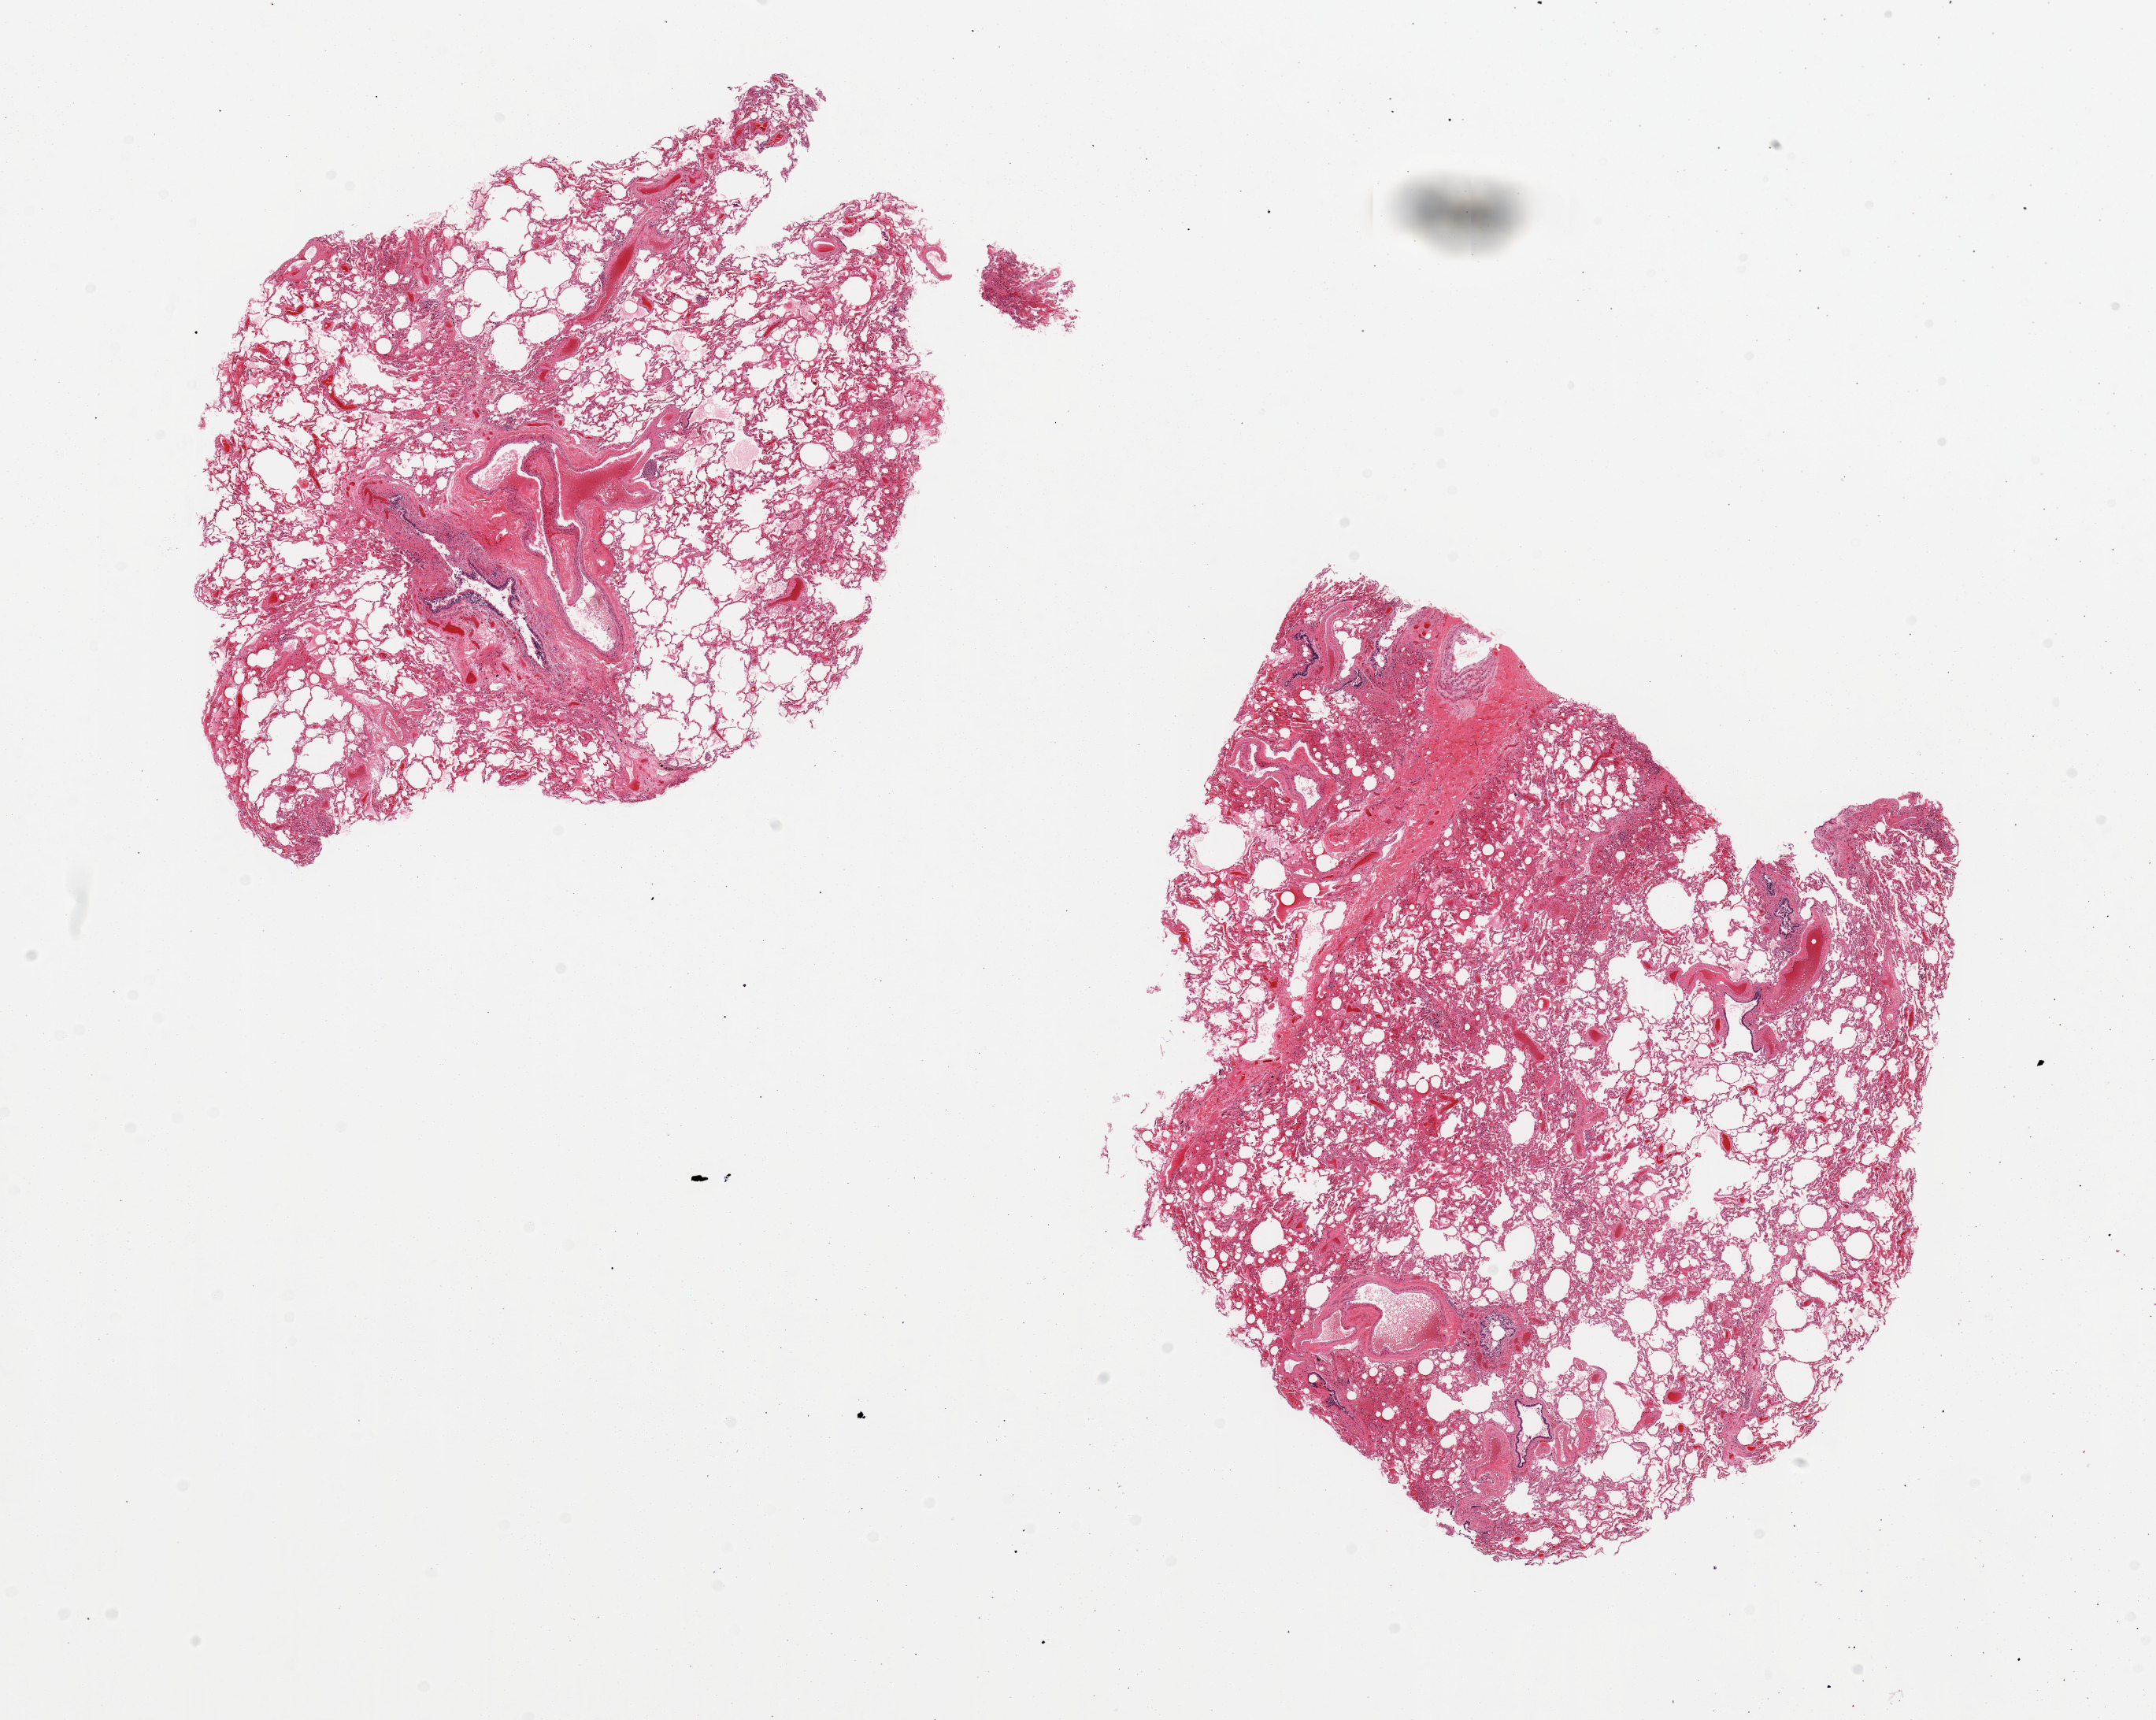
Whole-slide image, H&E stain, brightfield, whole scanned area (about 21.7 x 17.3 mm, from a 20x scan) shown as a low-resolution overview; PAXgene-fixed paraffin-embedded (PFPE) section; section of lung (target tissue); tissue donor sample.
Pathologist's review note for this sample: 2 pieces, minimal-mild congestion.